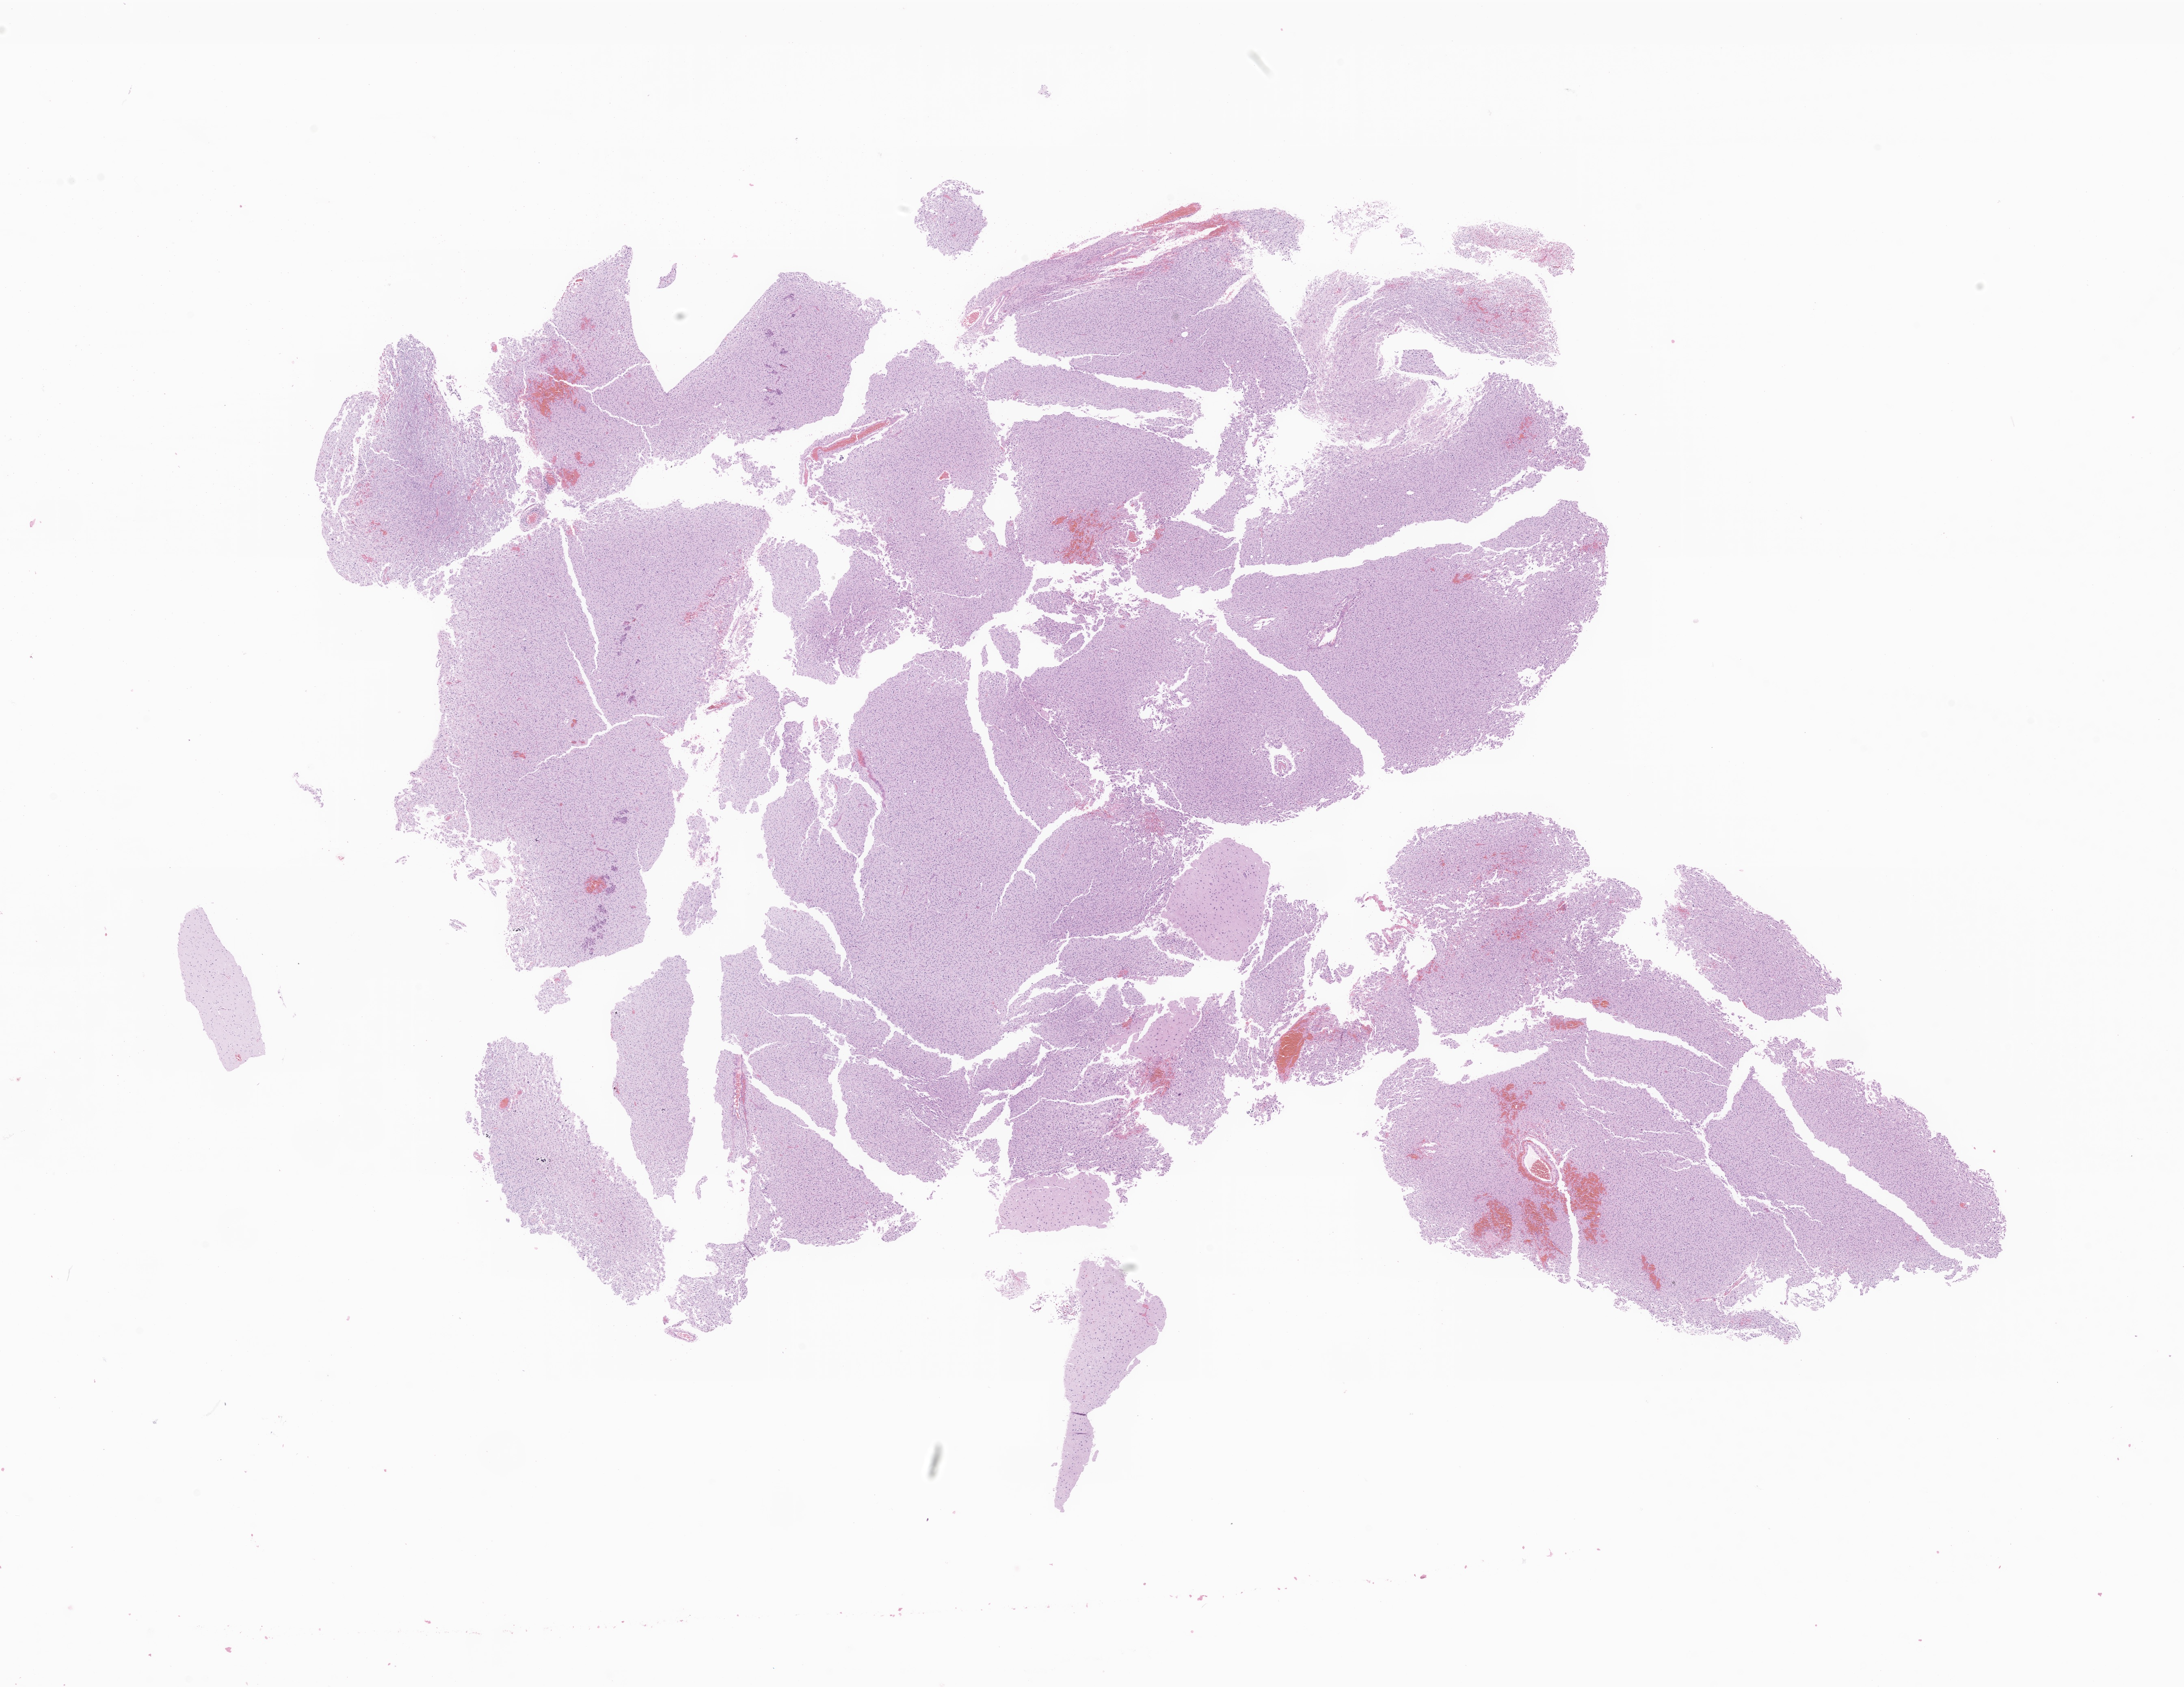
Digitized hematoxylin and eosin (H&E)-stained section of tumor tissue from the frontal lobe — low-resolution overview of the scanned area, about 22.7 x 17.5 mm; FFPE section. Patient: male, age 87 months (7 years 3 months).
Diagnosis (ICD-O-3 morphology term): Neoplasm, malignant.